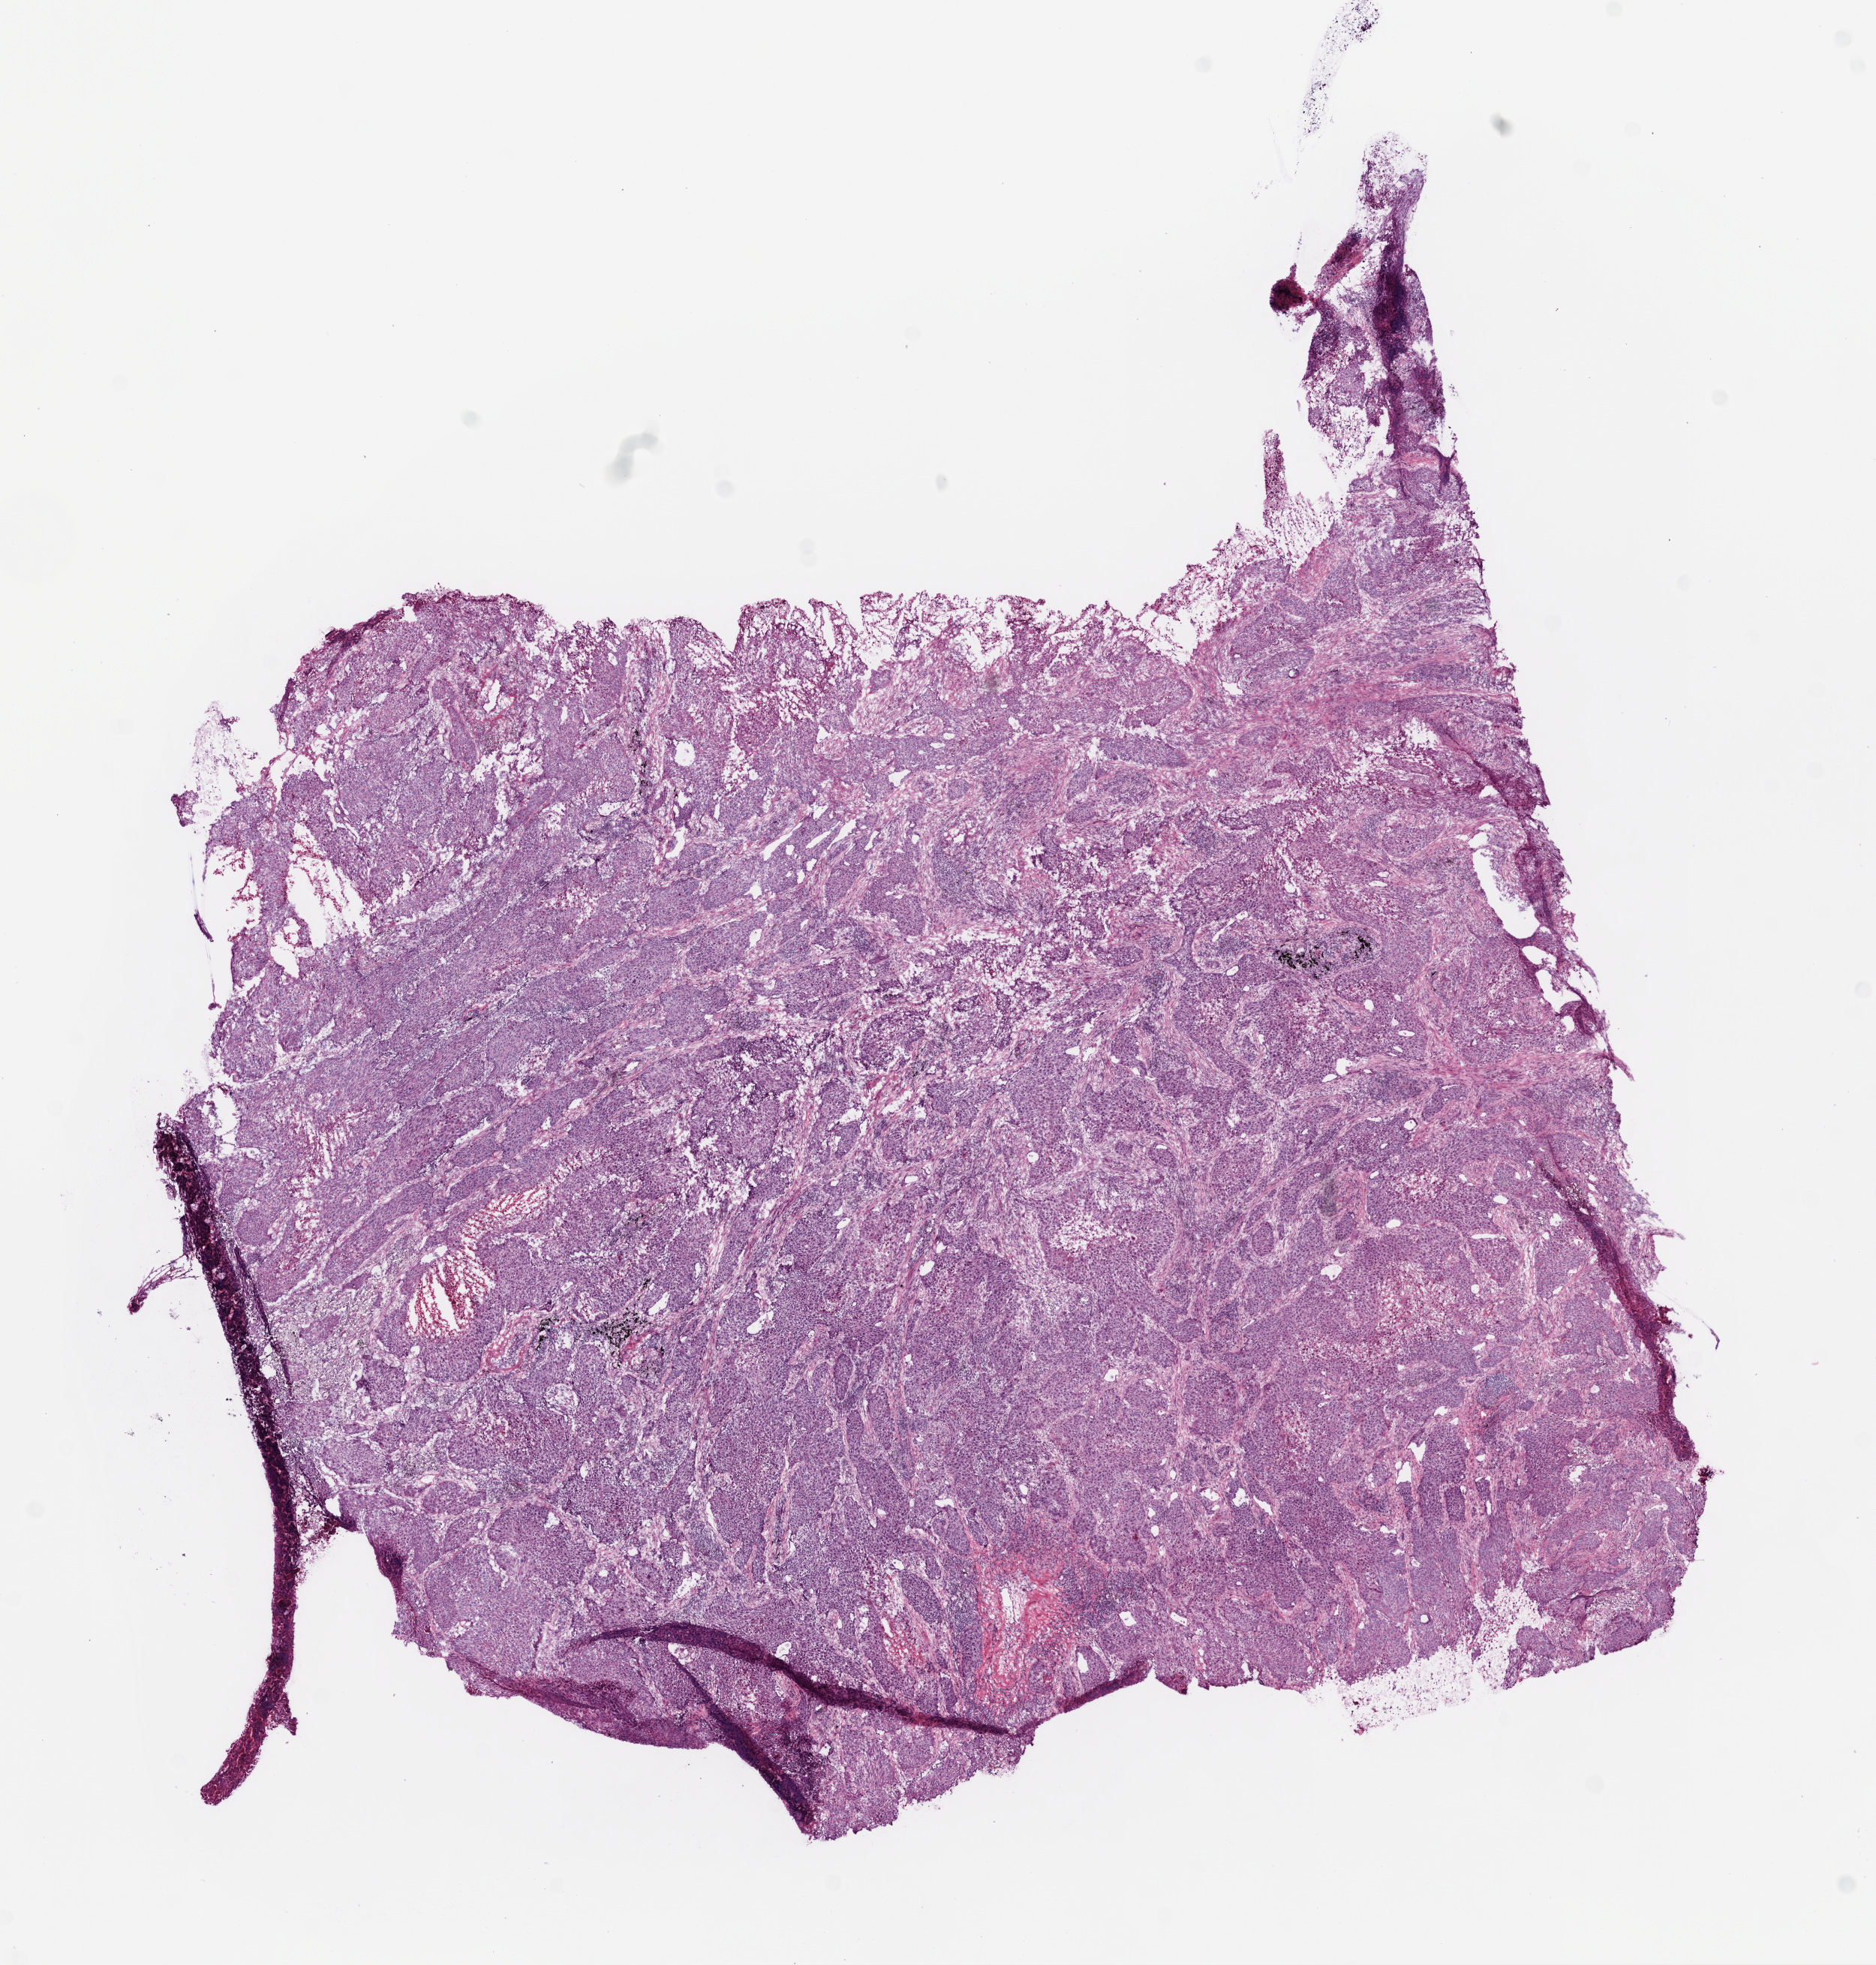
Digitized H&E tissue section (whole slide) — whole scanned area (about 10.0 x 10.5 mm) shown as a low-resolution overview, frozen section, sample: primary tumour, lung. Female, age 55 years at initial diagnosis. Composition of this section per pathologist review: tumour cells 85%, tumour nuclei 90%.
Diagnosis: Squamous cell carcinoma, NOS (lower lobe, lung).